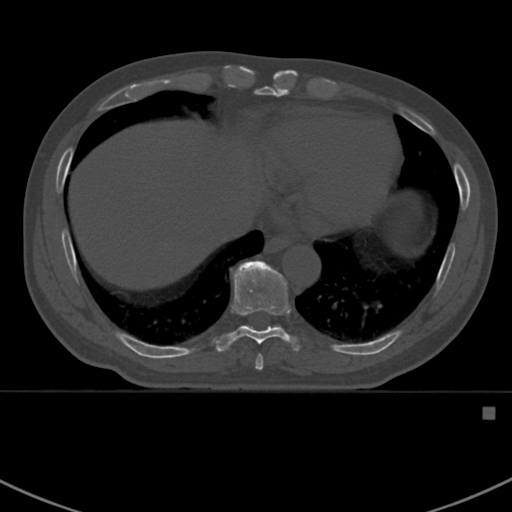
CT including the spine, one axial slice. Position 382 of 412 along the scan axis. Reconstruction kernel Br40s. Bone window (W 1800 / L 400 HU). 1.5 mm slice thickness. 512 × 512 image matrix, field of view 358 × 358 mm. Male patient, age 59 years. From the clinical record (not read from this slice): primary cancer: prostate.
Annotated regions visible in this slice (semi-automatically segmented with operator editing):
- T8 vertebra: bounding box (x1, y1, x2, y2) in pixels: (255, 355, 263, 371)
- T9 vertebra: (217, 260, 299, 352)